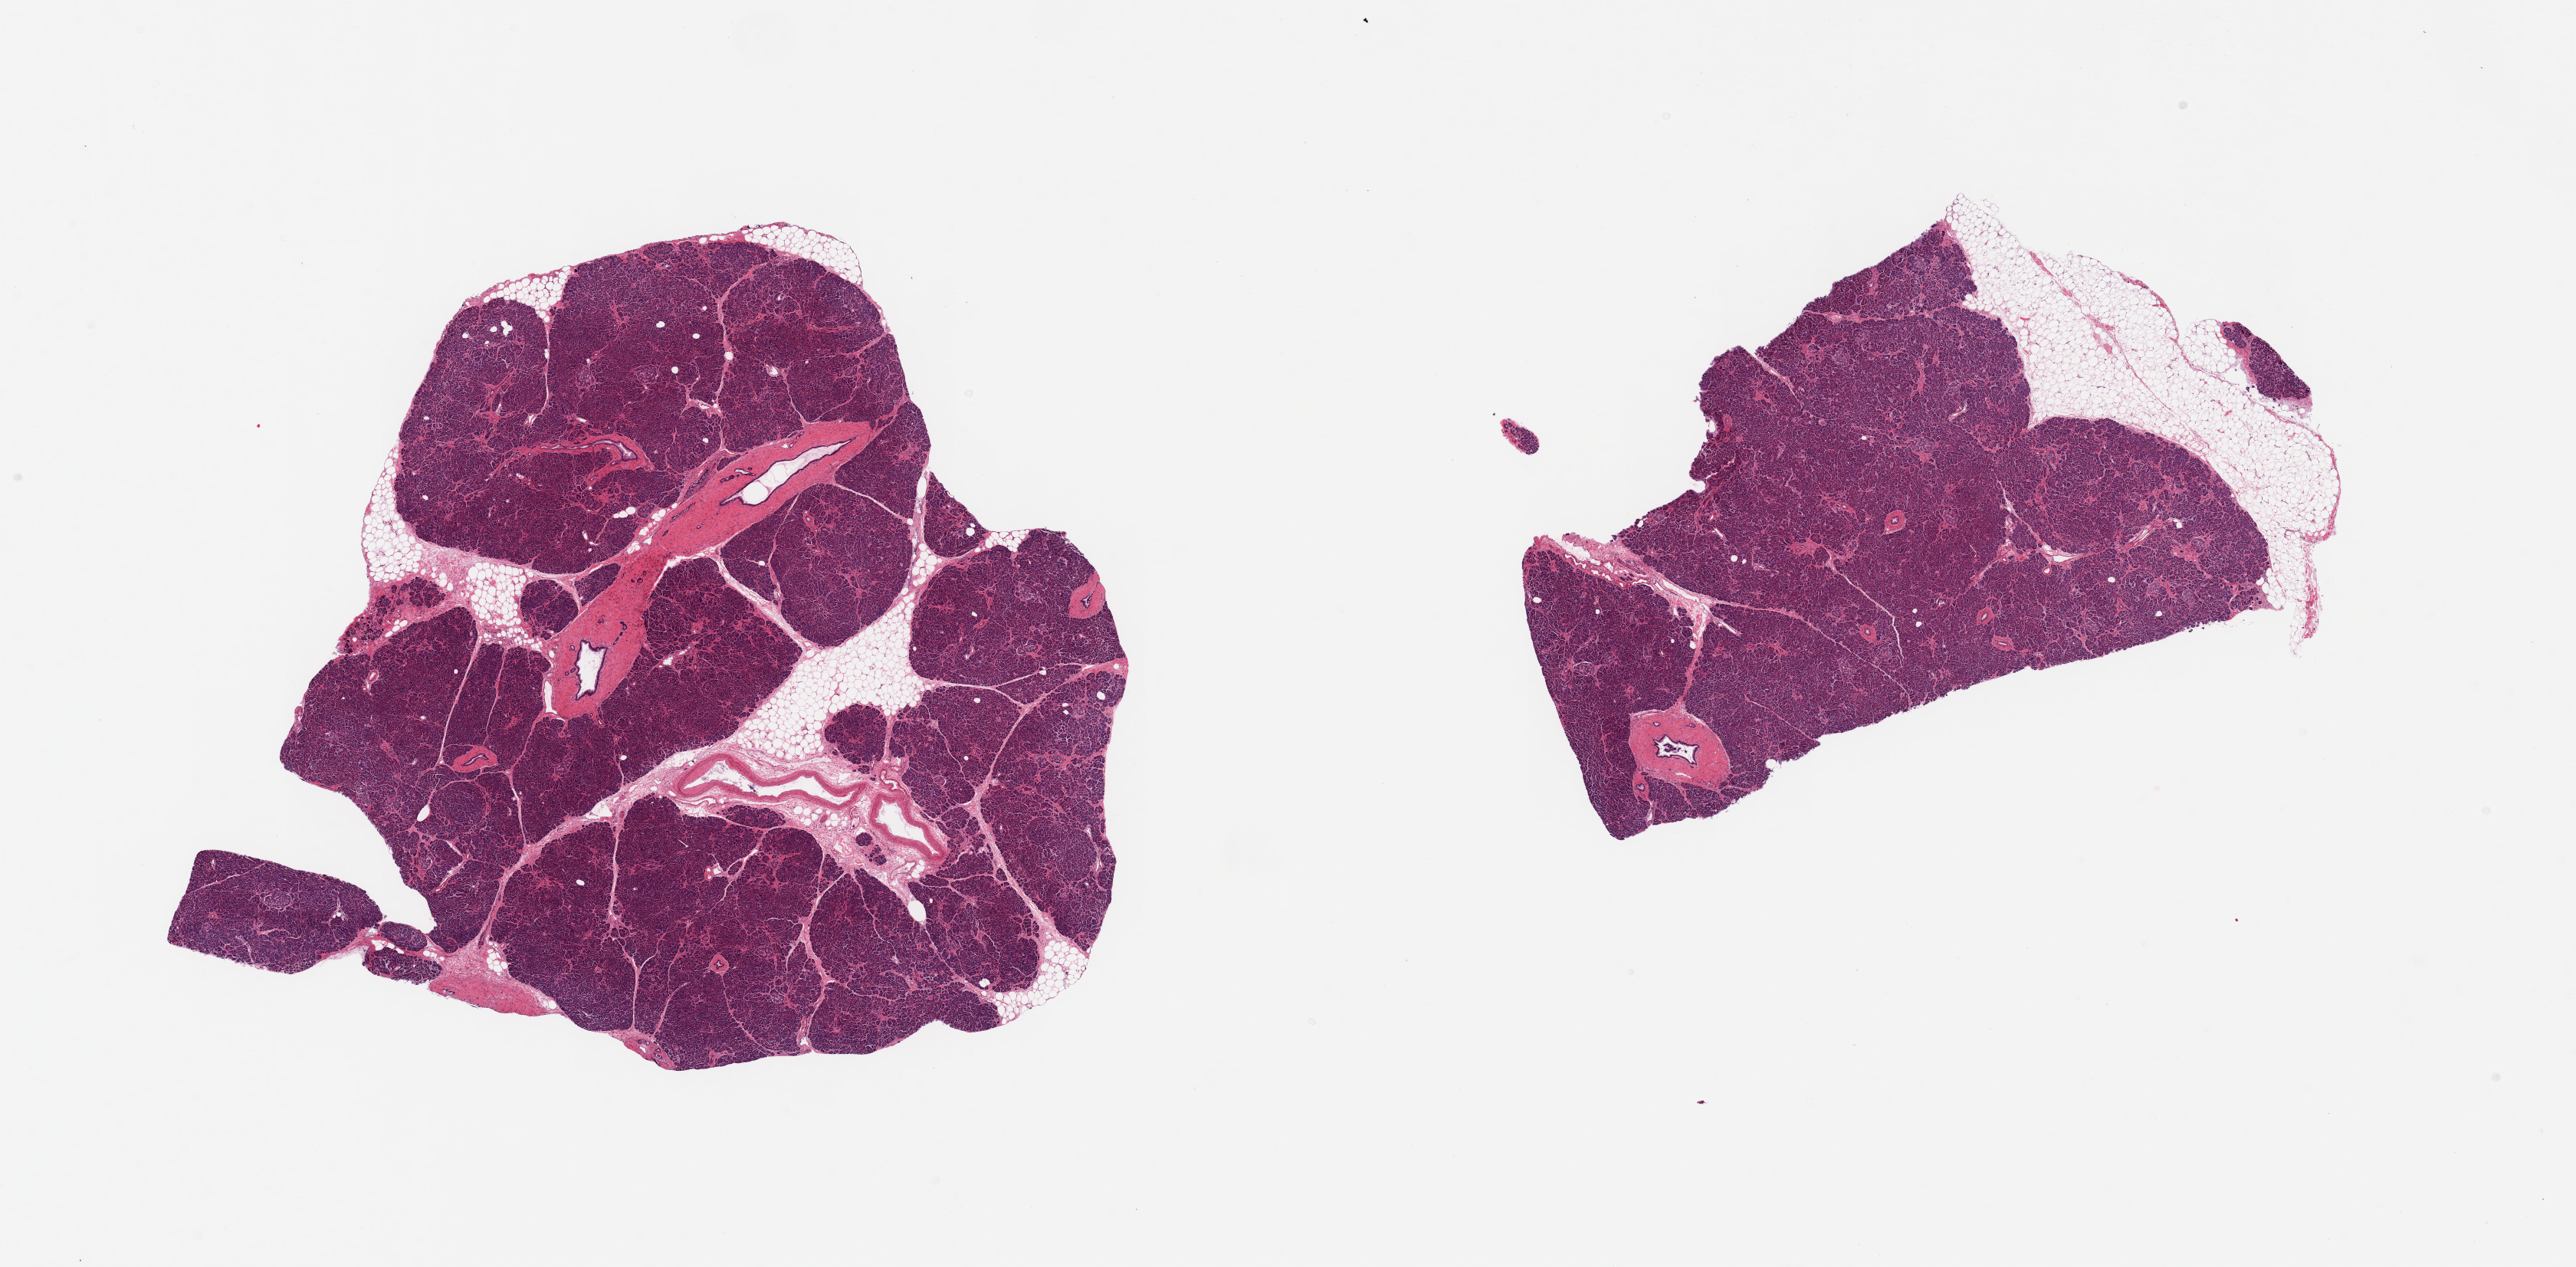
Hematoxylin and eosin (H&E) whole-slide image, low-resolution overview of the scanned area, about 26.6 x 13.1 mm (slide scanned at 20x), PAXgene-fixed paraffin-embedded (PFPE) section, target tissue: pancreas, tissue donor sample. Male donor.
* pathologist's review note for this sample: 2 pieces, islets well-preserved; small edge of adherent fat, 1.5-2mm